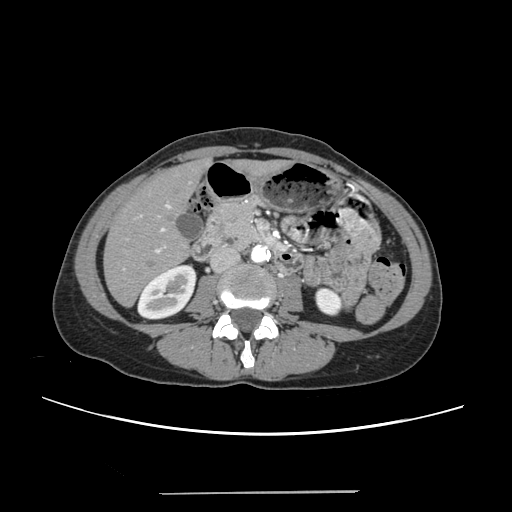
Contrast-enhanced abdominal CT, one axial slice. Slice 85 of 240 in the series (ordered by position). Intravenous contrast given. Soft-tissue window (W 400 / L 40 HU). 512 × 512 image matrix. Female patient, age 60 years. From the clinical record (not read from this slice): diagnosis: colorectal cancer liver metastases, imaged before liver resection; multiple liver metastases: no; largest metastasis: 1.5 cm; disease in both lobes: no.
Outlined on this slice (outlined manually by an expert reader):
- liver: bounding box [x1, y1, x2, y2] px = [105, 163, 276, 305]
- planned liver remnant (the part of the liver to remain after resection): [105, 164, 275, 305]
- portal vein (with intrahepatic branches): [123, 204, 170, 269]